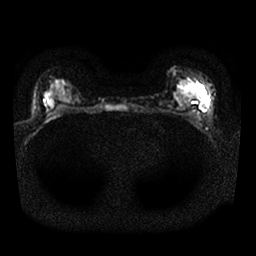
Breast MRI, one axial slice. Position 12 of 25 along the scan axis. Diffusion-weighted series; image 2 of 4 stored at this slice position (different b-values; order by instance number). 1.5 T. 4 mm slice thickness. 256 × 256 image matrix. Female patient.
Annotated regions visible in this slice (expert manual segmentation):
- tumour on diffusion-weighted imaging: box from (x=200, y=96) to (x=209, y=108) px